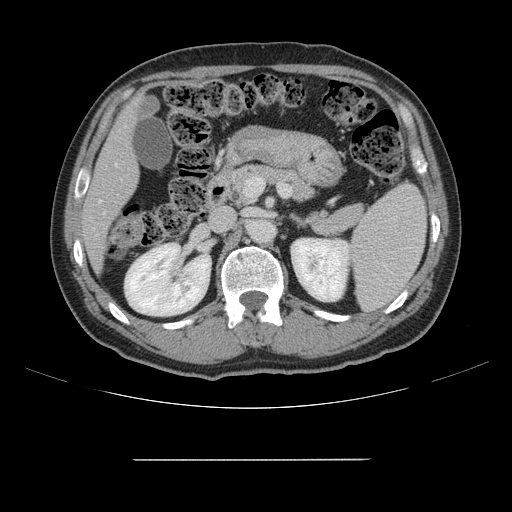
Contrast-enhanced abdominal CT, one axial slice; position 73 of 164 along the scan axis; intravenous contrast given; soft-tissue window (W 400 / L 40 HU); 2.5 mm slice thickness; 512 × 512 image matrix, field of view 404 × 404 mm. Male patient, age 54 years. Case-level facts recorded for this patient, not image findings: diagnosis: colorectal cancer liver metastases, imaged before liver resection.
Annotated regions visible in this slice (outlined manually by an expert reader):
- hepatic veins: bounding box [x1, y1, x2, y2] px = [98, 164, 118, 203]
- liver: [85, 103, 138, 268]
- planned liver remnant (the part of the liver to remain after resection): [85, 104, 138, 268]